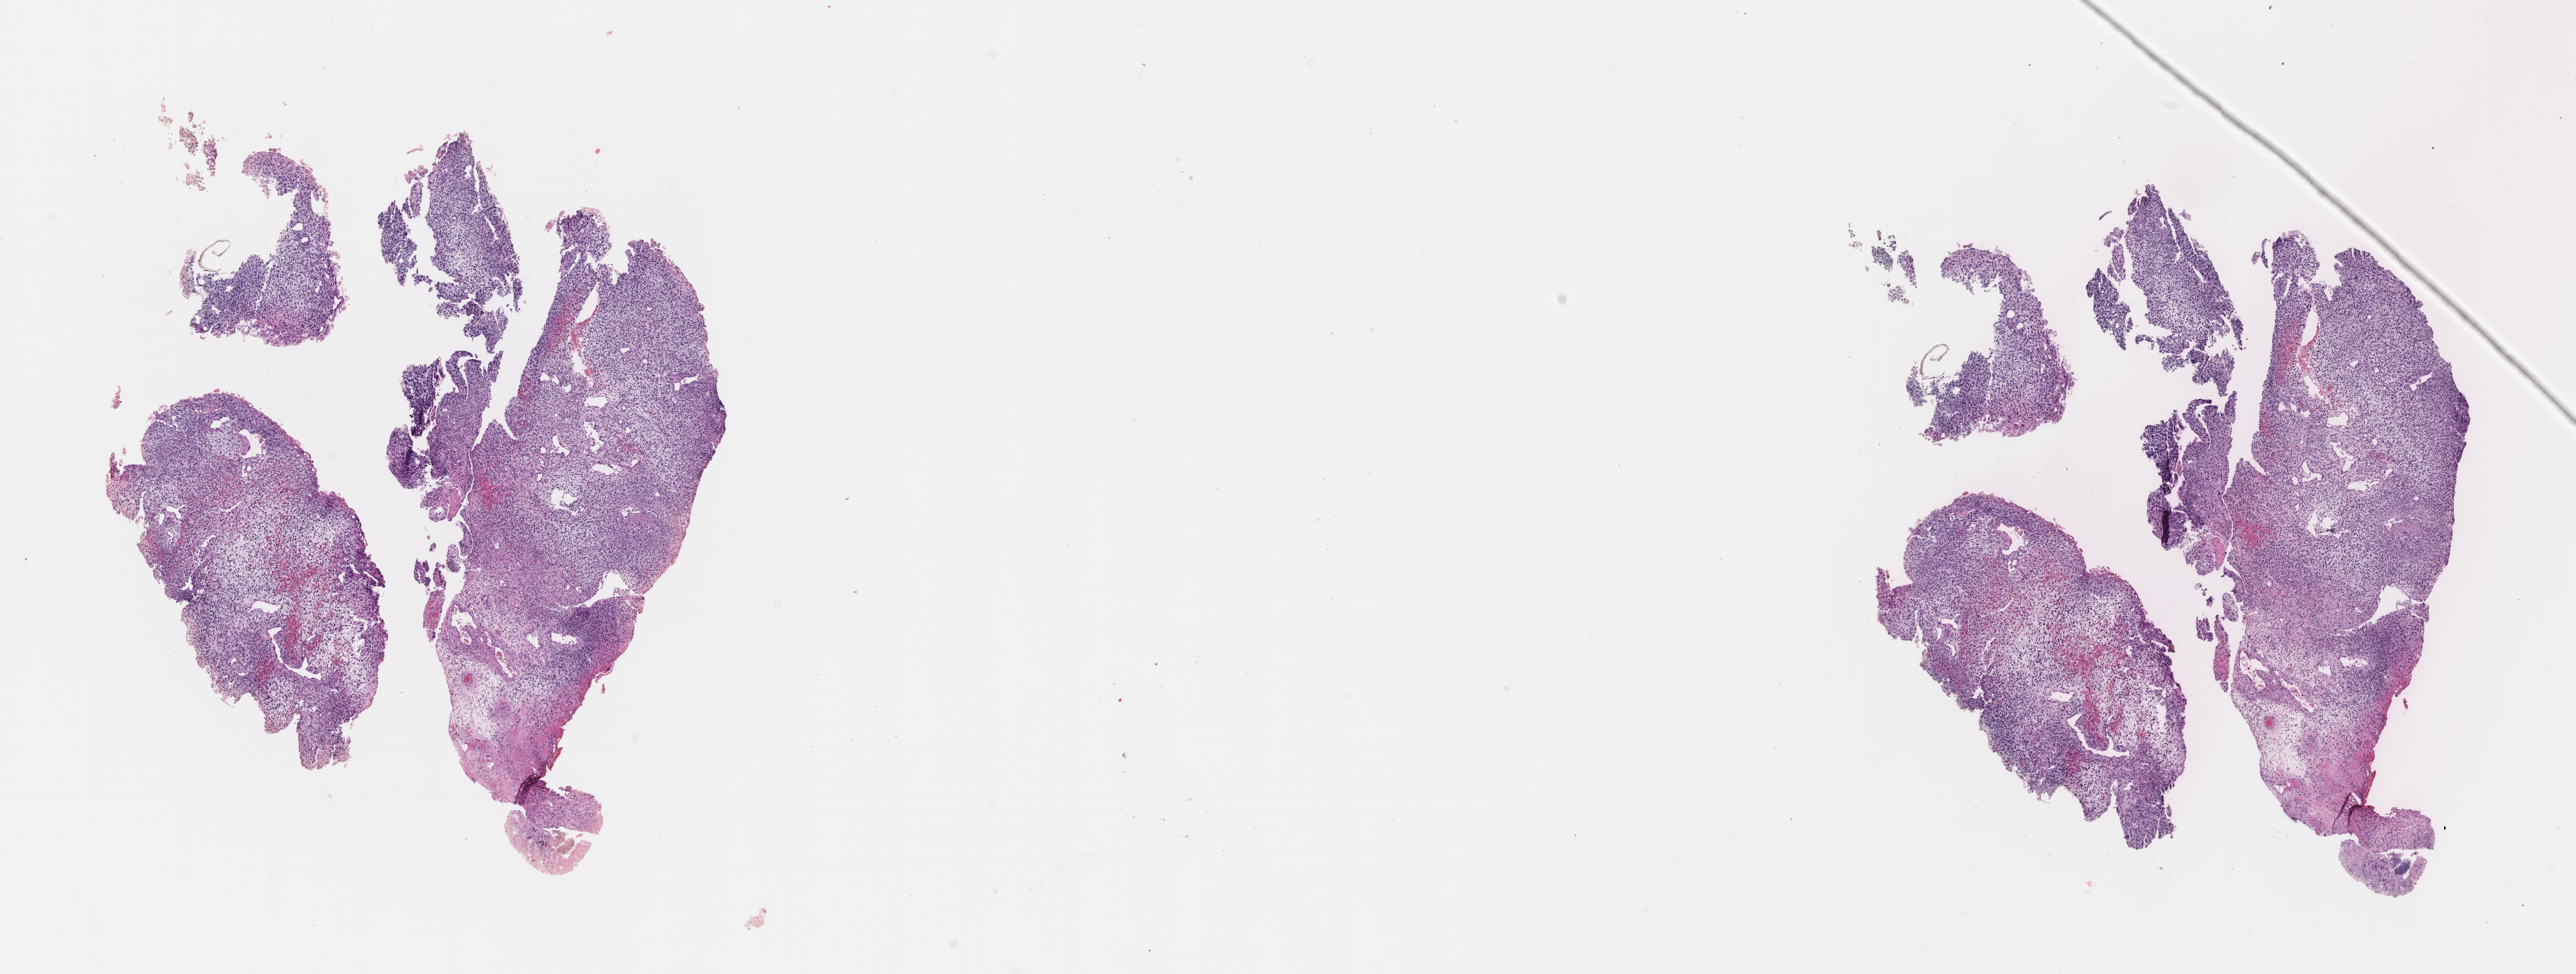
Hematoxylin and eosin (H&E) whole-slide image of tumor tissue — whole scanned area (about 14.6 x 5.5 mm) shown as a low-resolution overview; FFPE section. Male patient, age at diagnosis 15.8 years.
- diagnosis: rhabdomyosarcoma; histological classification: embryonal rhabdomyosarcoma